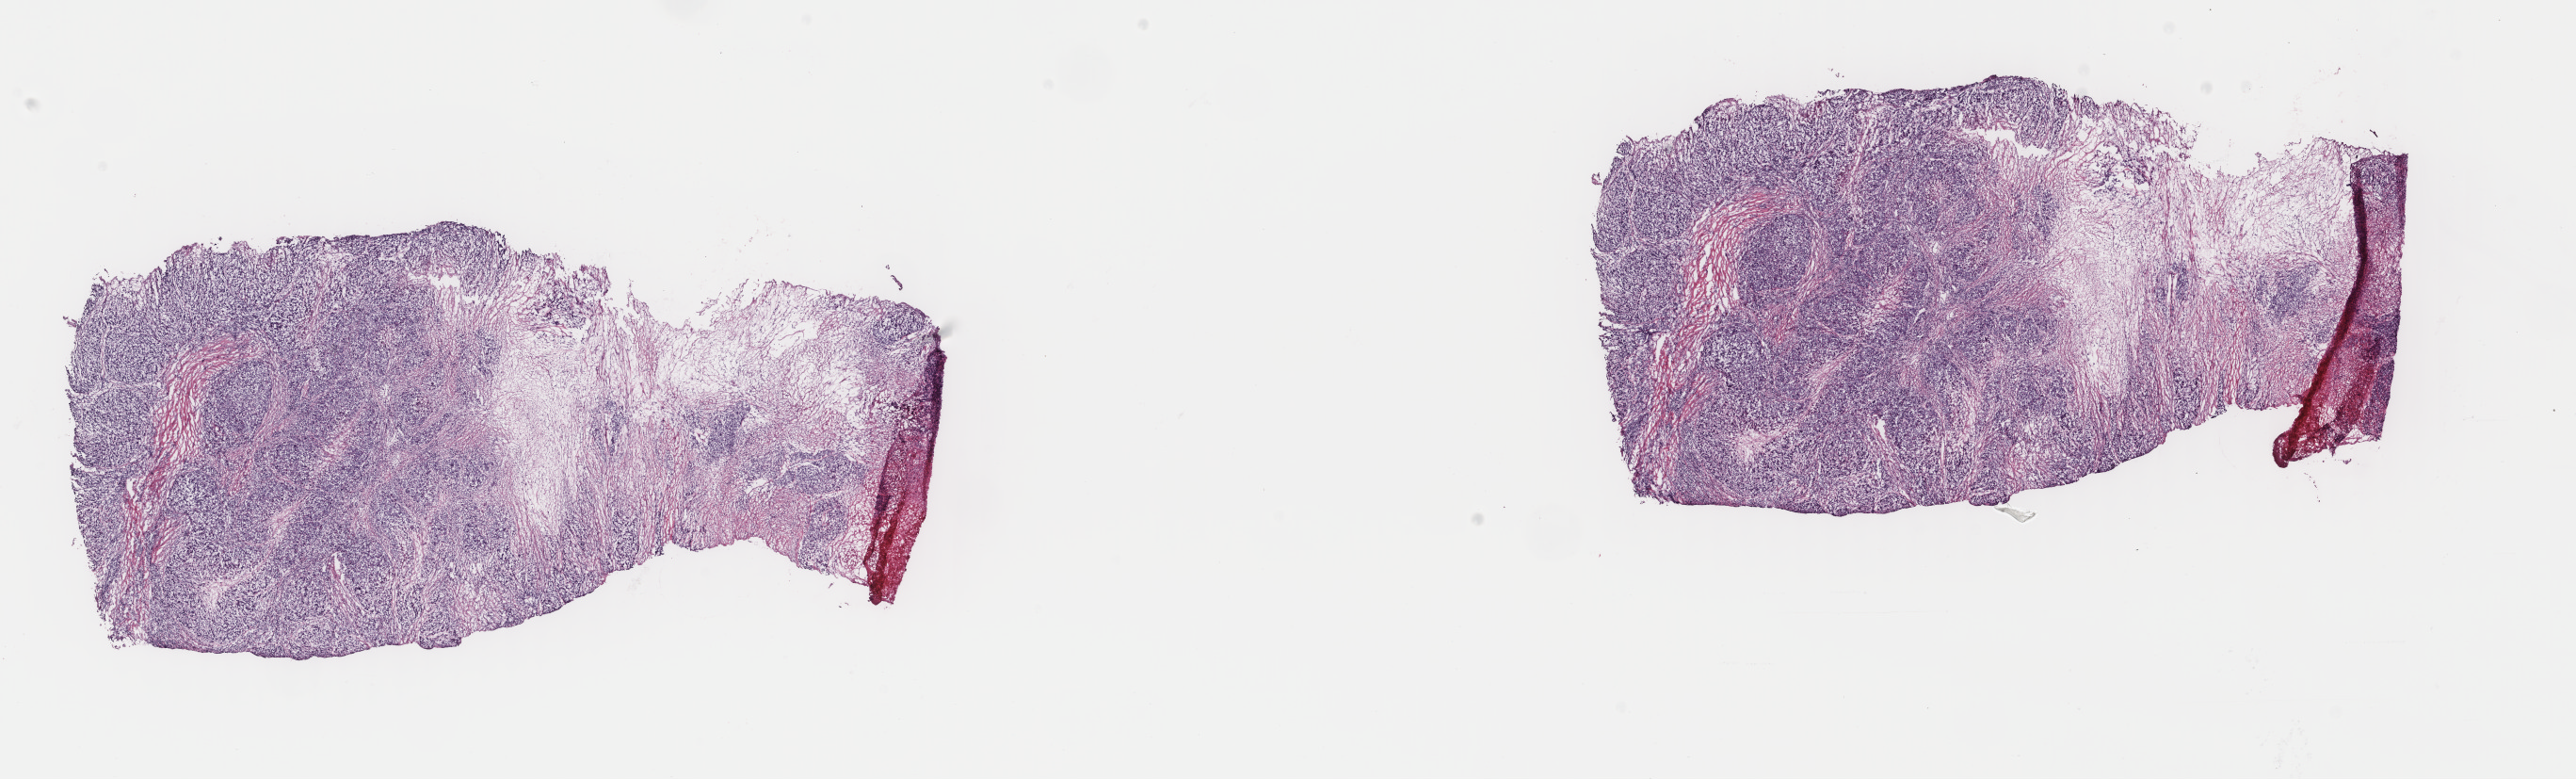
Whole-slide histology image, H&E-stained — whole scanned area (about 21.7 x 6.6 mm, acquisition: 40x scan) shown as a low-resolution overview; frozen section from the top of the tissue portion; metastatic tumour sample, sampled site: skin of upper limb and shoulder. Patient: female, age at initial diagnosis 59 years. Slide review estimates, as recorded: tumour cells 85%, tumour nuclei 75%, normal cells 0%, stromal cells 15%, necrosis 0%. Inflammatory infiltration, as recorded: lymphocyte infiltration 0%, monocyte infiltration 0%, neutrophil infiltration 0%.
* this section: metastatic tumour tissue
* patient diagnosis: Malignant melanoma, NOS